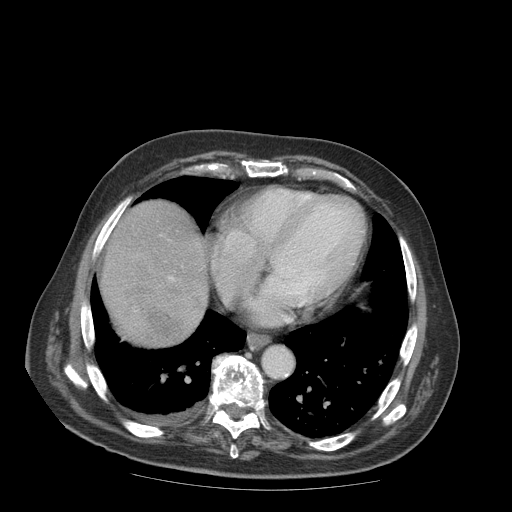
Contrast-enhanced abdominal CT (liver protocol), one axial slice. Reconstruction kernel STANDARD. Soft-tissue window (W 400 / L 40 HU). 2.5 mm slice thickness. 512 × 512 image matrix. From the clinical record (not read from this slice): diagnosis: hepatocellular carcinoma (patient treated with transarterial chemoembolisation; whether this scan precedes or follows treatment is not stated here); TNM stage (as recorded): Stage-IIIB; Child-Pugh class: A; tumour differentiation: well differentiated; tumour nodularity: multinodular.
Structures marked on this image (semi-automatically segmented with operator editing):
- abdominal aorta: box from (x=261, y=346) to (x=293, y=377) px
- liver parenchyma outside the tumour (the mass and vessels are separate outlines, so this box may not span the whole liver): (x=100, y=200)–(x=206, y=346)
- mass: (x=100, y=238)–(x=204, y=345)
- liver vessels: (x=170, y=277)–(x=174, y=280)